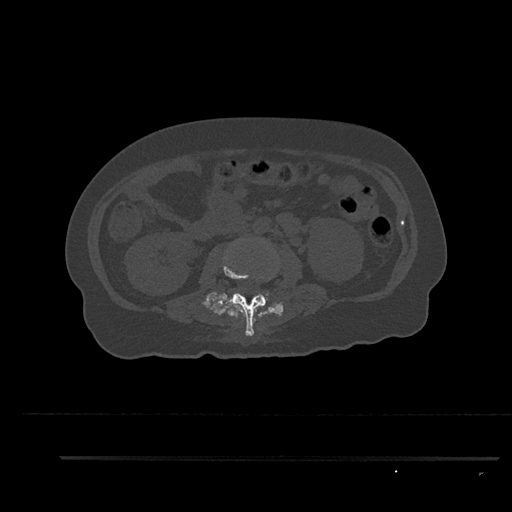
CT including the spine, one axial slice; reconstruction kernel Br40s/3; bone window (W 1800 / L 400 HU); 0.5 mm slice thickness; 512 × 512 image matrix, field of view 408 × 408 mm. Patient: female, 44 years. Case-level facts recorded for this patient, not image findings: primary cancer: renal; vertebrae with lytic lesions (as recorded): L1.
Annotated regions visible in this slice (semi-automatically segmented with operator editing):
- L2 vertebra: bounding box [x1, y1, x2, y2] px = [224, 261, 266, 336]
- L3 vertebra: [225, 292, 269, 302]